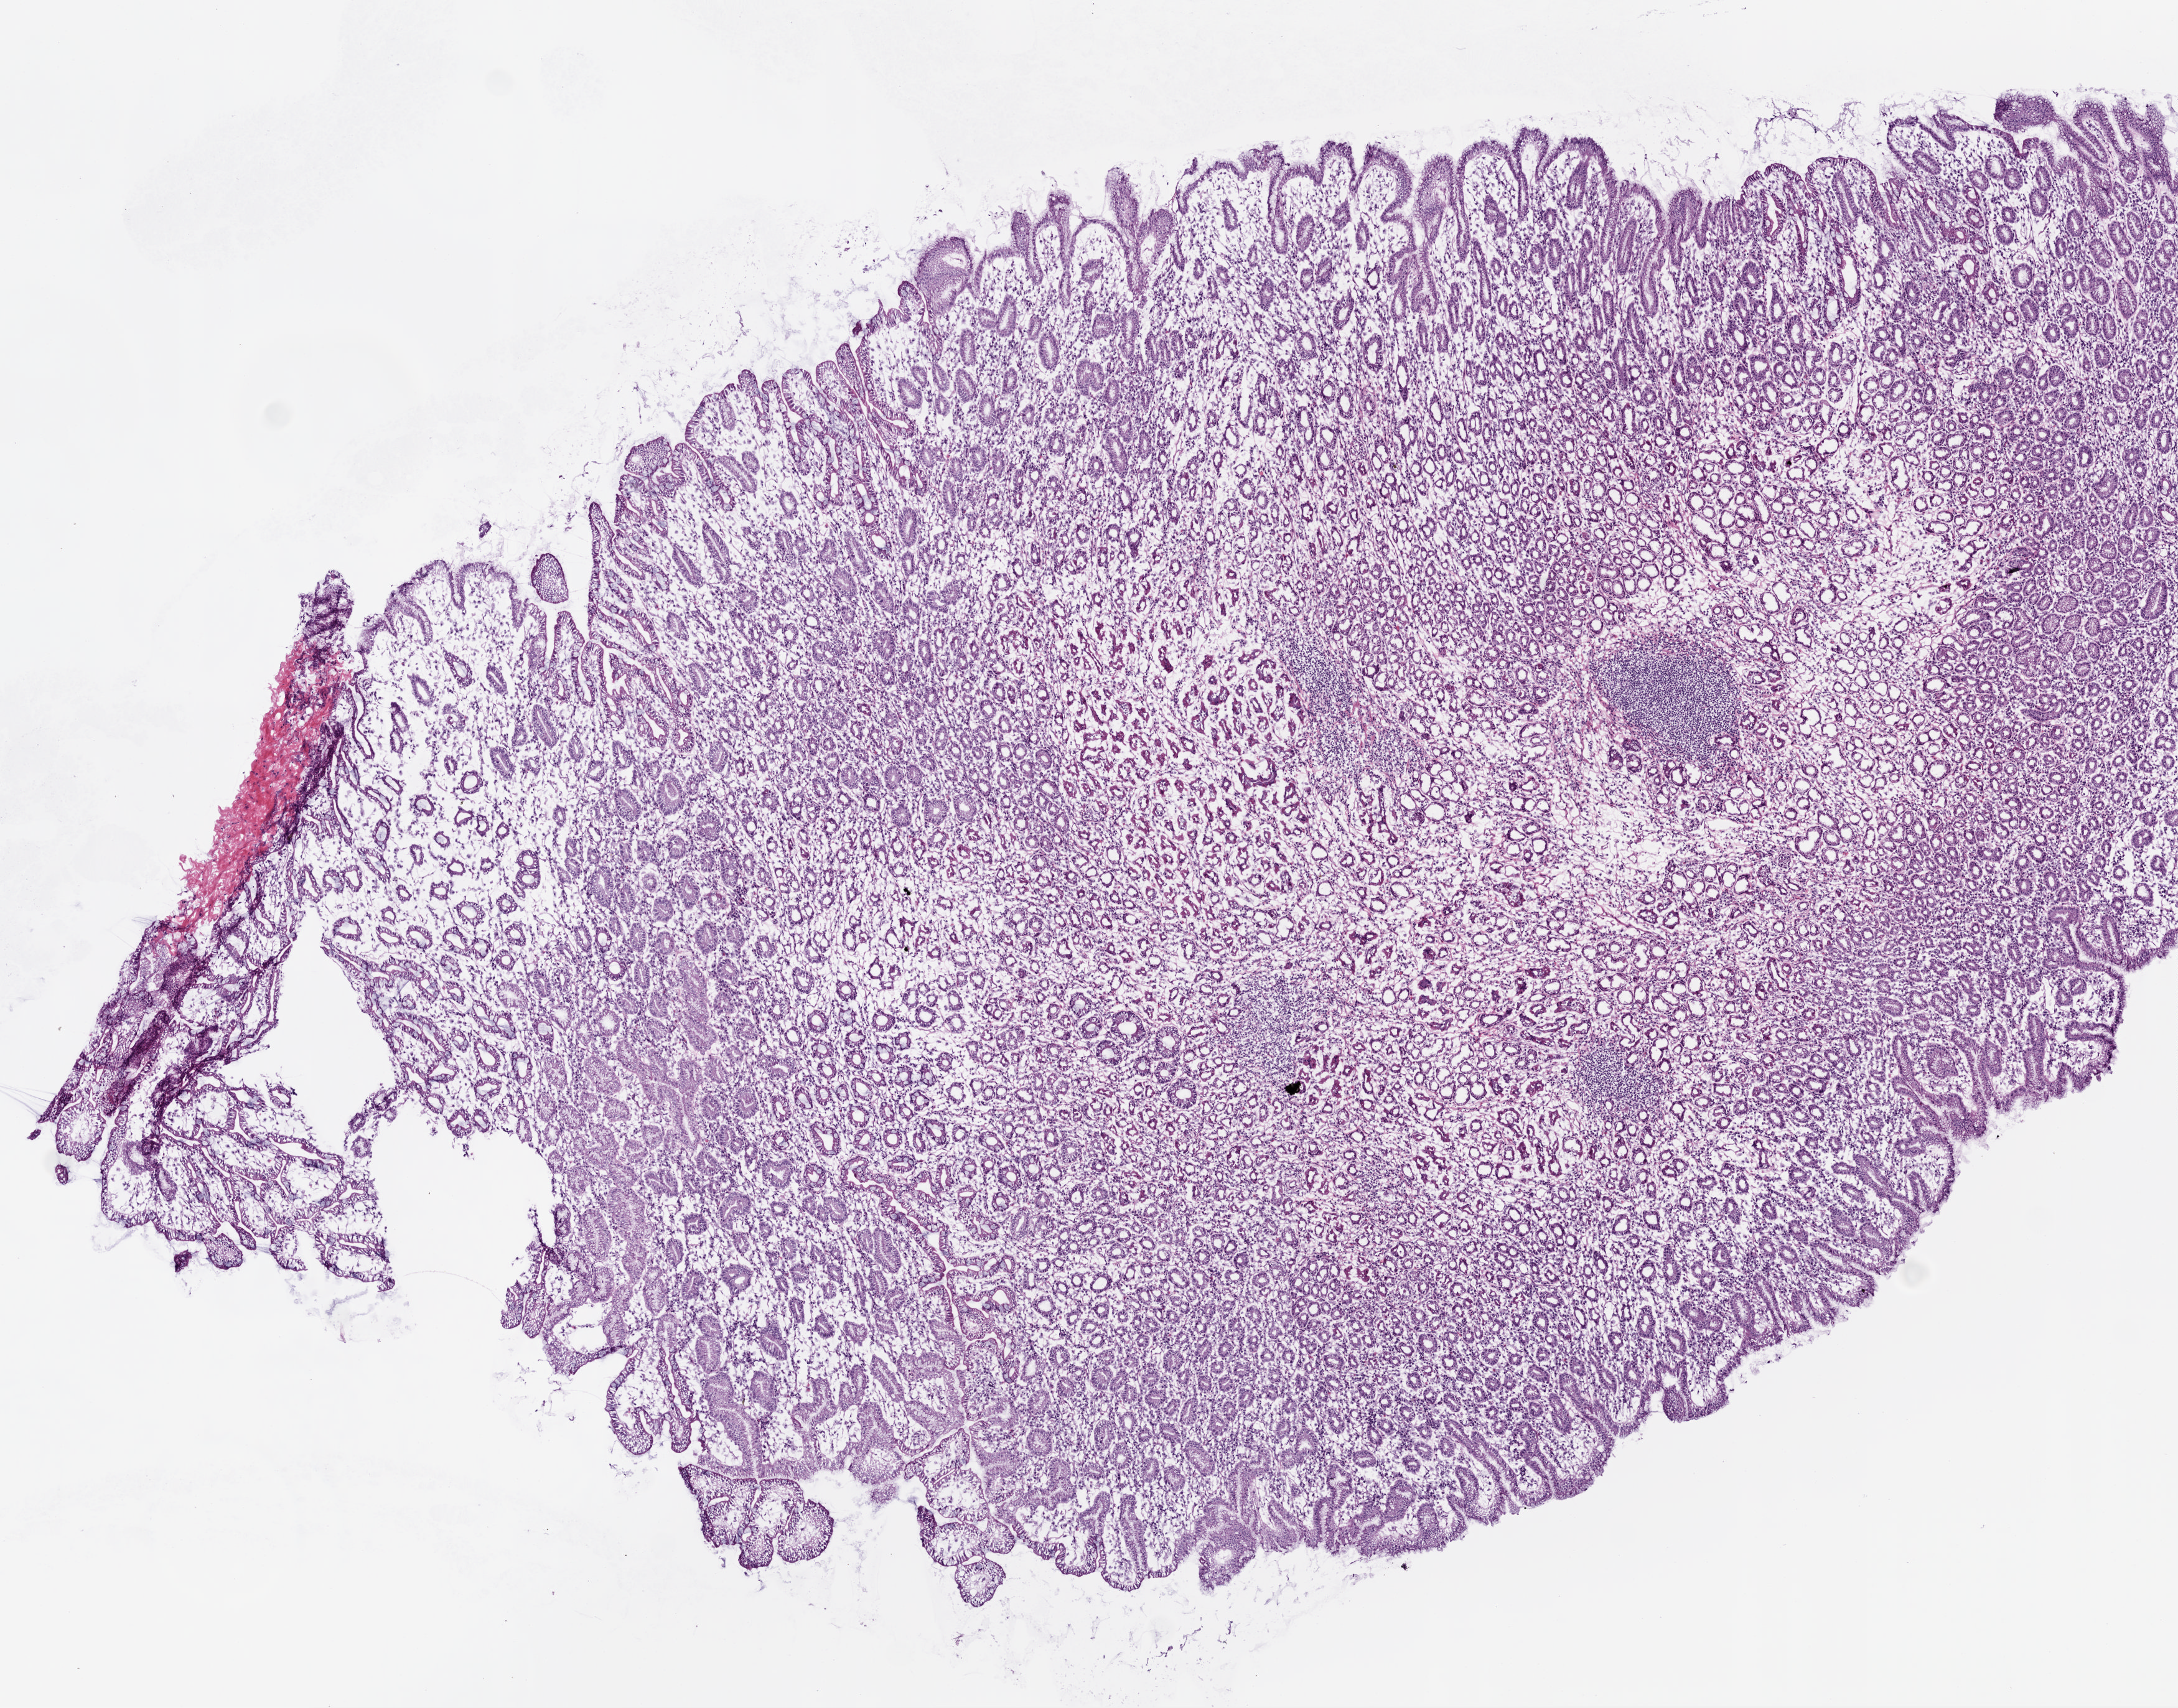
H&E whole-slide image, shown as a low-resolution overview of the whole scanned area (about 7.0 x 5.5 mm), frozen section, sample: solid tissue normal (non-tumour tissue), stomach. Patient: male, age at initial diagnosis 71 years.
- this section: solid tissue normal (non-tumour) sample from the same patient
- patient diagnosis: Adenocarcinoma, NOS (cardia, NOS)